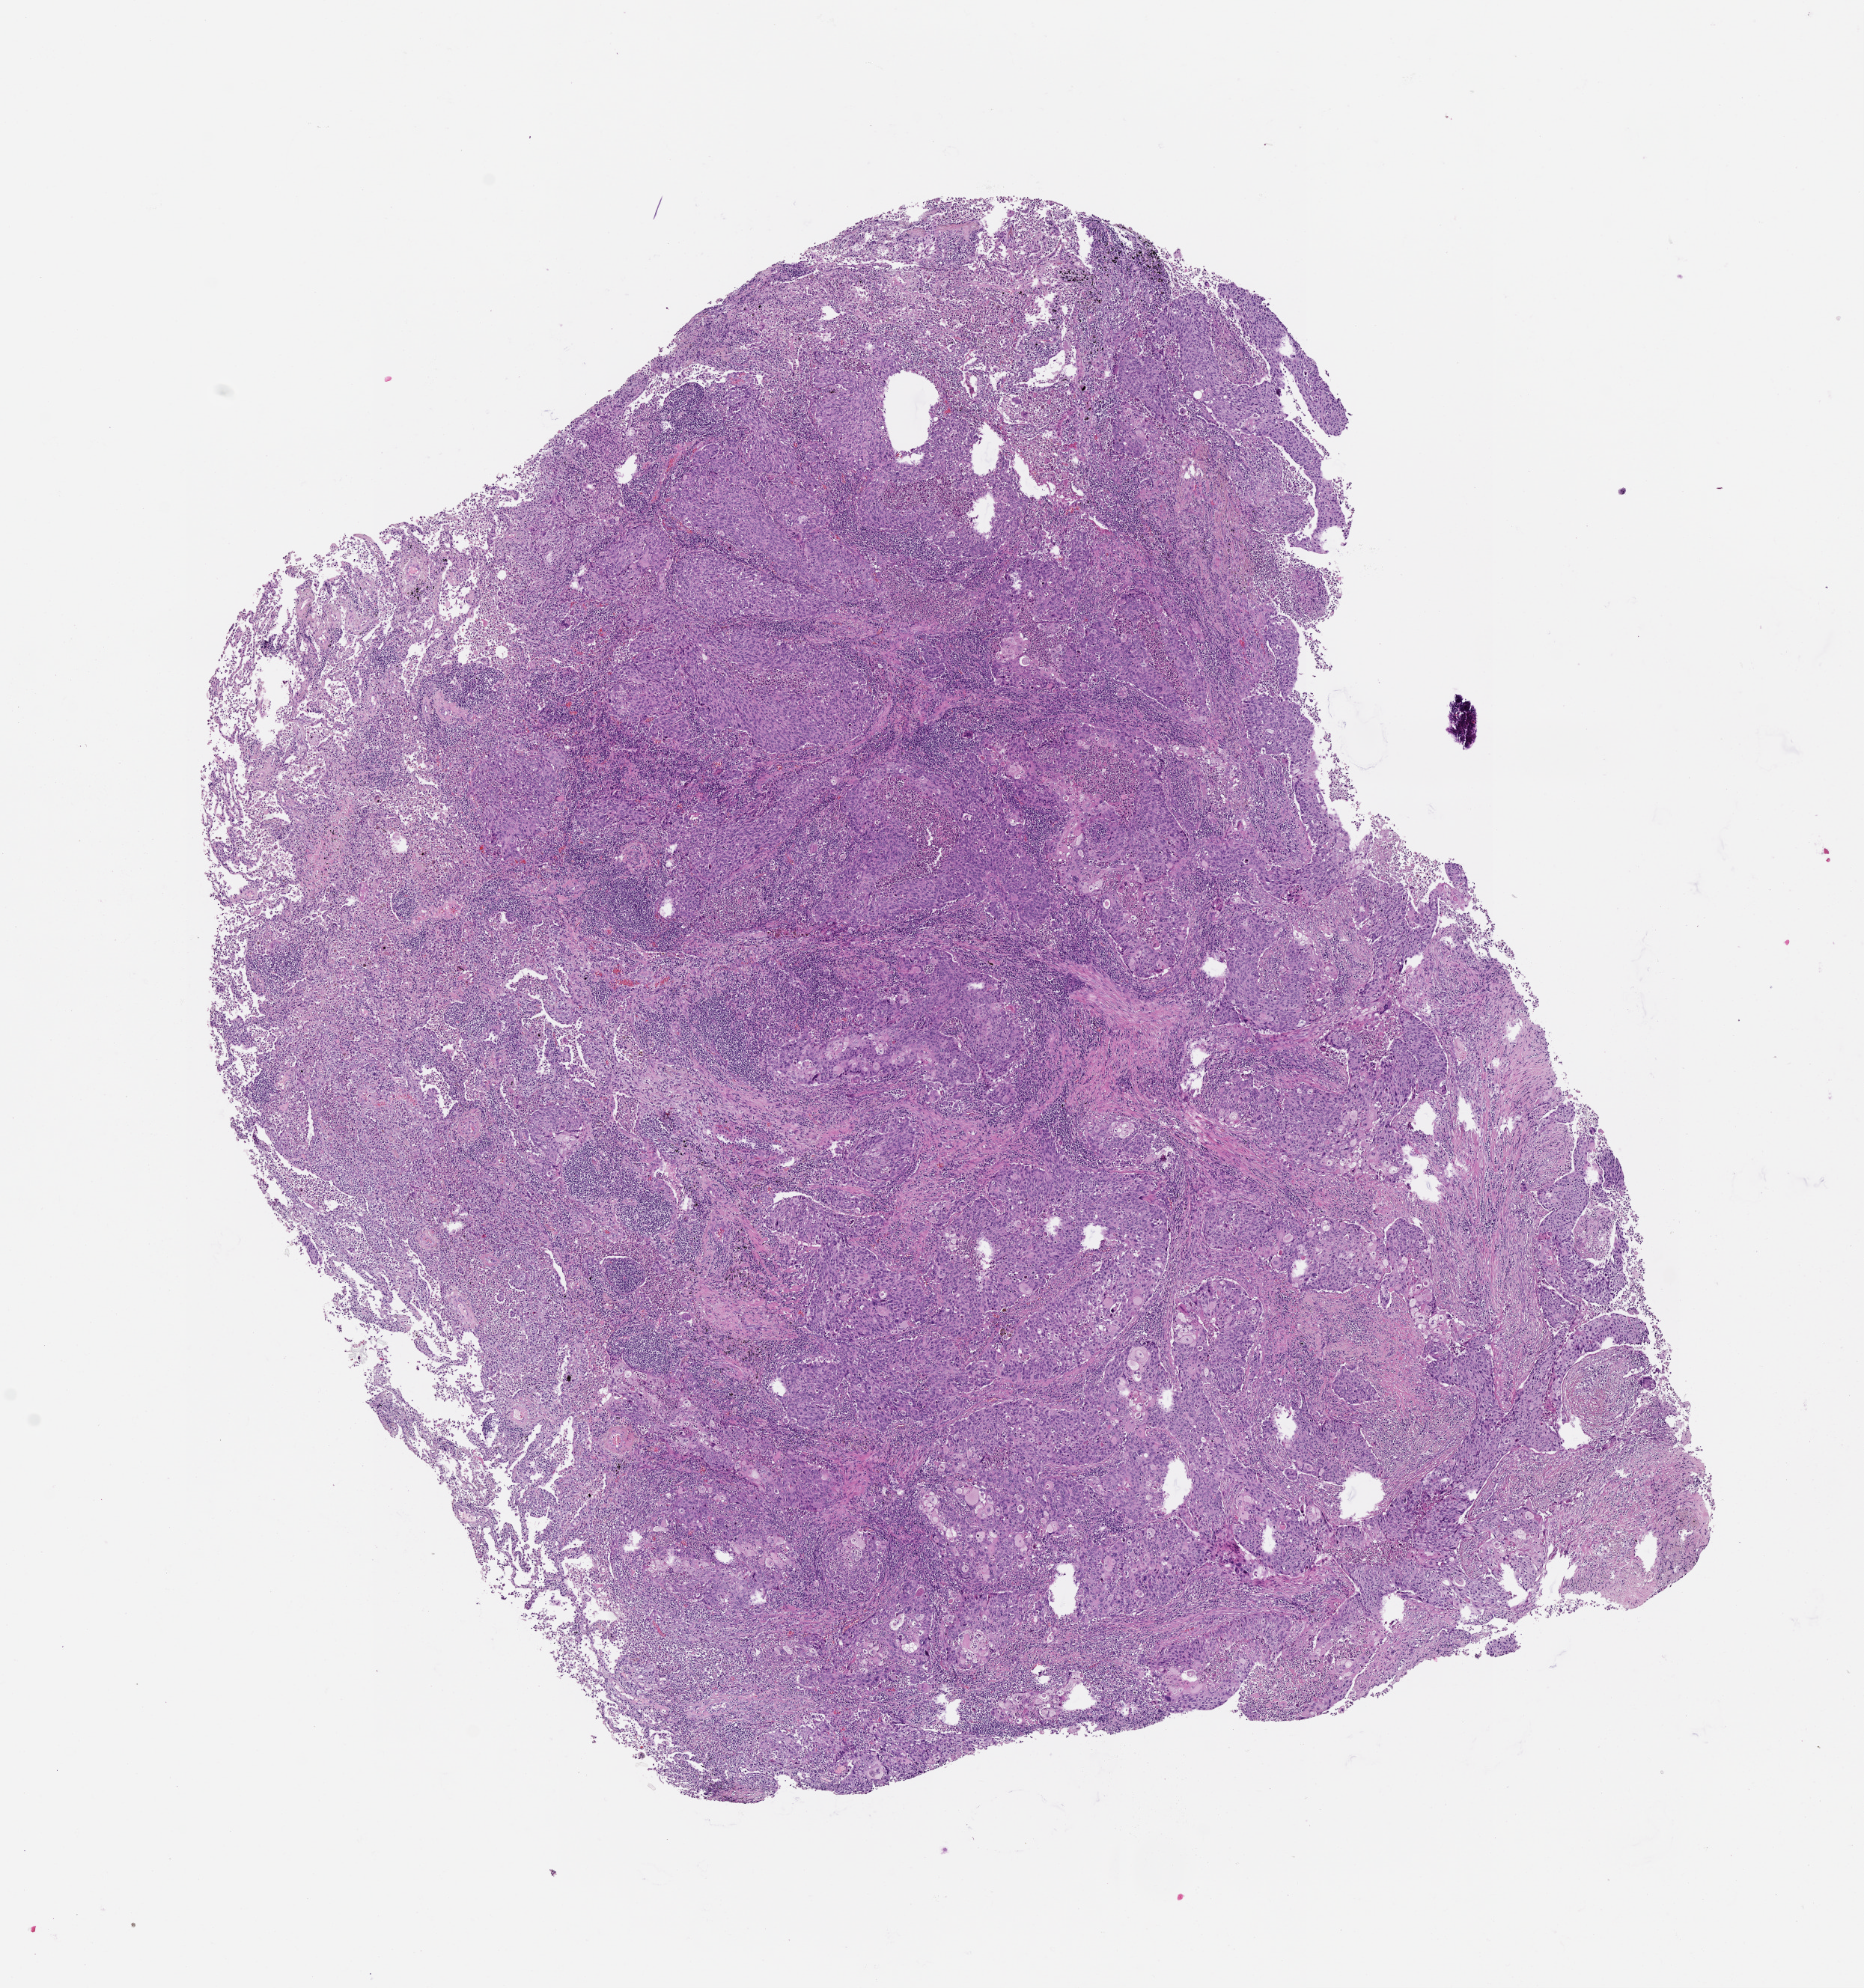
Whole-slide histology image, H&E — whole scanned area (about 10.0 x 10.7 mm) shown as a low-resolution overview; tumour tissue sample, lung. 64-year-old male patient.
Patient diagnosis (cohort enrolment): squamous cell carcinoma (lung).